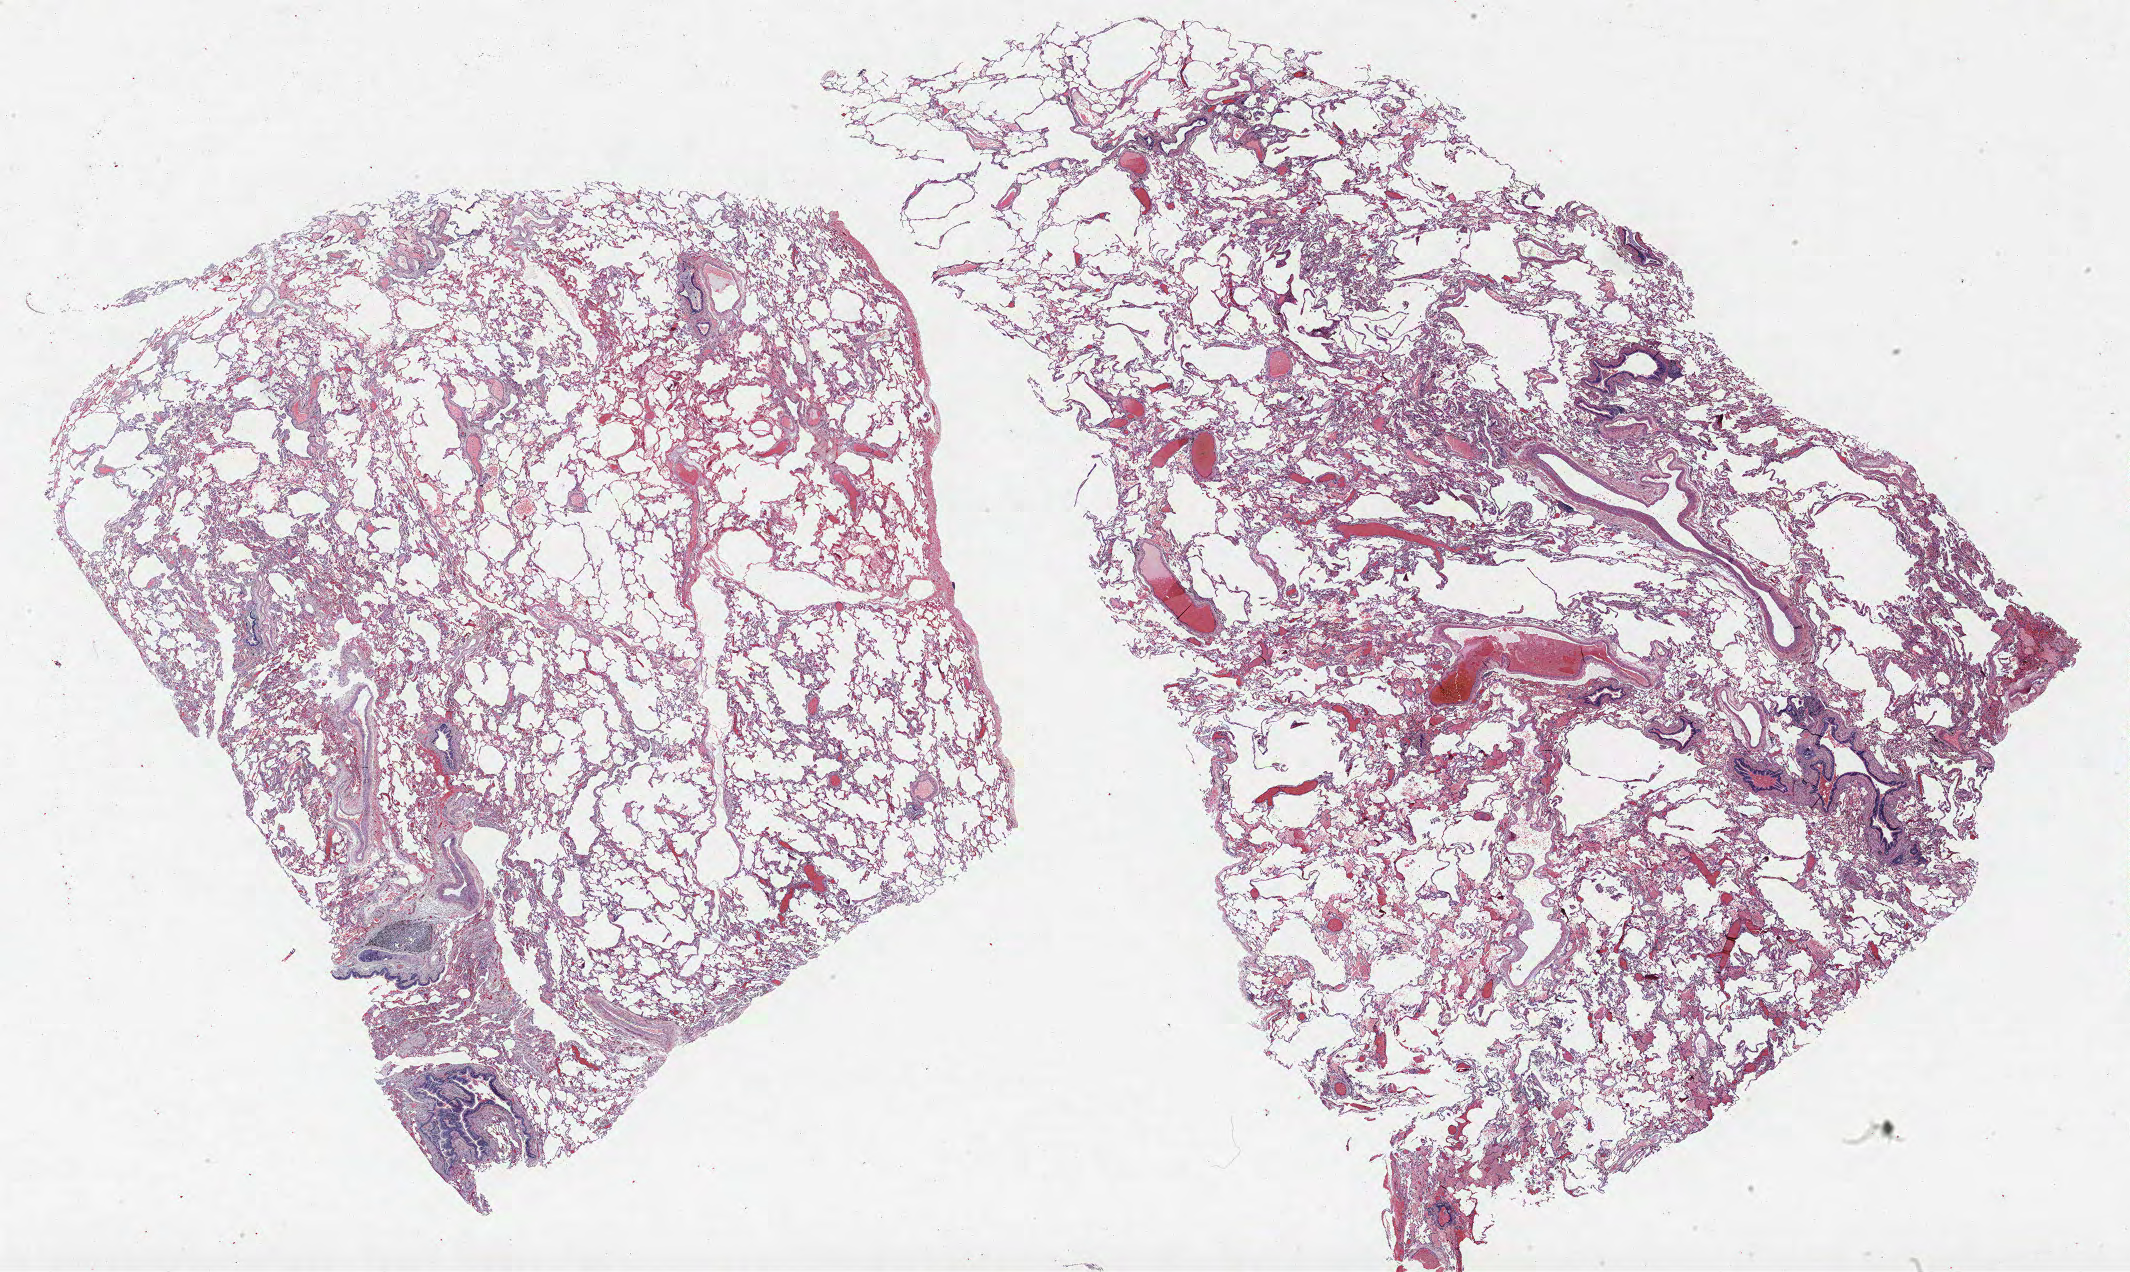
Hematoxylin and eosin (H&E) stained whole-slide image — whole scanned area (about 34.1 x 20.4 mm) shown as a low-resolution overview, FFPE section, lung. Male patient, aged 59 at enrolment. Current smoker at enrolment.
Participant's lung-cancer diagnosis: Non-small cell carcinoma (ICD-O-3 8046/3). Stage (AJCC 6th edition): IA. Primary tumour location (clinical record): right upper lobe. Tumour size (pathology): 13 mm. ICD-O-3 topography: upper lobe of lung (C34.1).